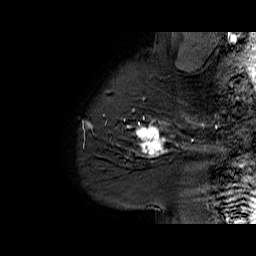
Breast MRI (dynamic contrast-enhanced), one sagittal slice. Slice 52 of 60 in the series (ordered by position). Dynamic contrast-enhanced series, time point 2 of 6 at this slice position (early post-contrast). 1.5 T. TE 6.1 ms, TR 32.9 ms. 256 × 256 image matrix. Female patient. Case-level facts recorded for this patient, not image findings: setting: breast cancer imaged before/during neoadjuvant chemotherapy; receptor status: HER2-positive.
Structures marked on this image (semi-automatic segmentation, software-assisted and operator-edited):
- analysis volume of interest (the breast-tissue region the enhancement analysis was run in; not a lesion): box from (x=127, y=95) to (x=194, y=165) px
- tumour enhancement mask (voxels above the 100 % enhancement threshold inside the analysis volume of interest): (x=127, y=98)–(x=193, y=156)